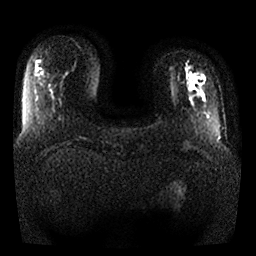
Breast MRI, one axial slice. Position 5 of 25 along the scan axis. Diffusion-weighted series; image 2 of 4 stored at this slice position (different b-values; order by instance number). 1.5 T. 4 mm slice thickness. 256 × 256 image matrix, field of view 340 × 340 mm. Female patient.
Outlined on this slice (expert manual segmentation):
- tumour on diffusion-weighted imaging: bounding box (x1, y1, x2, y2) in pixels: (189, 76, 196, 89)